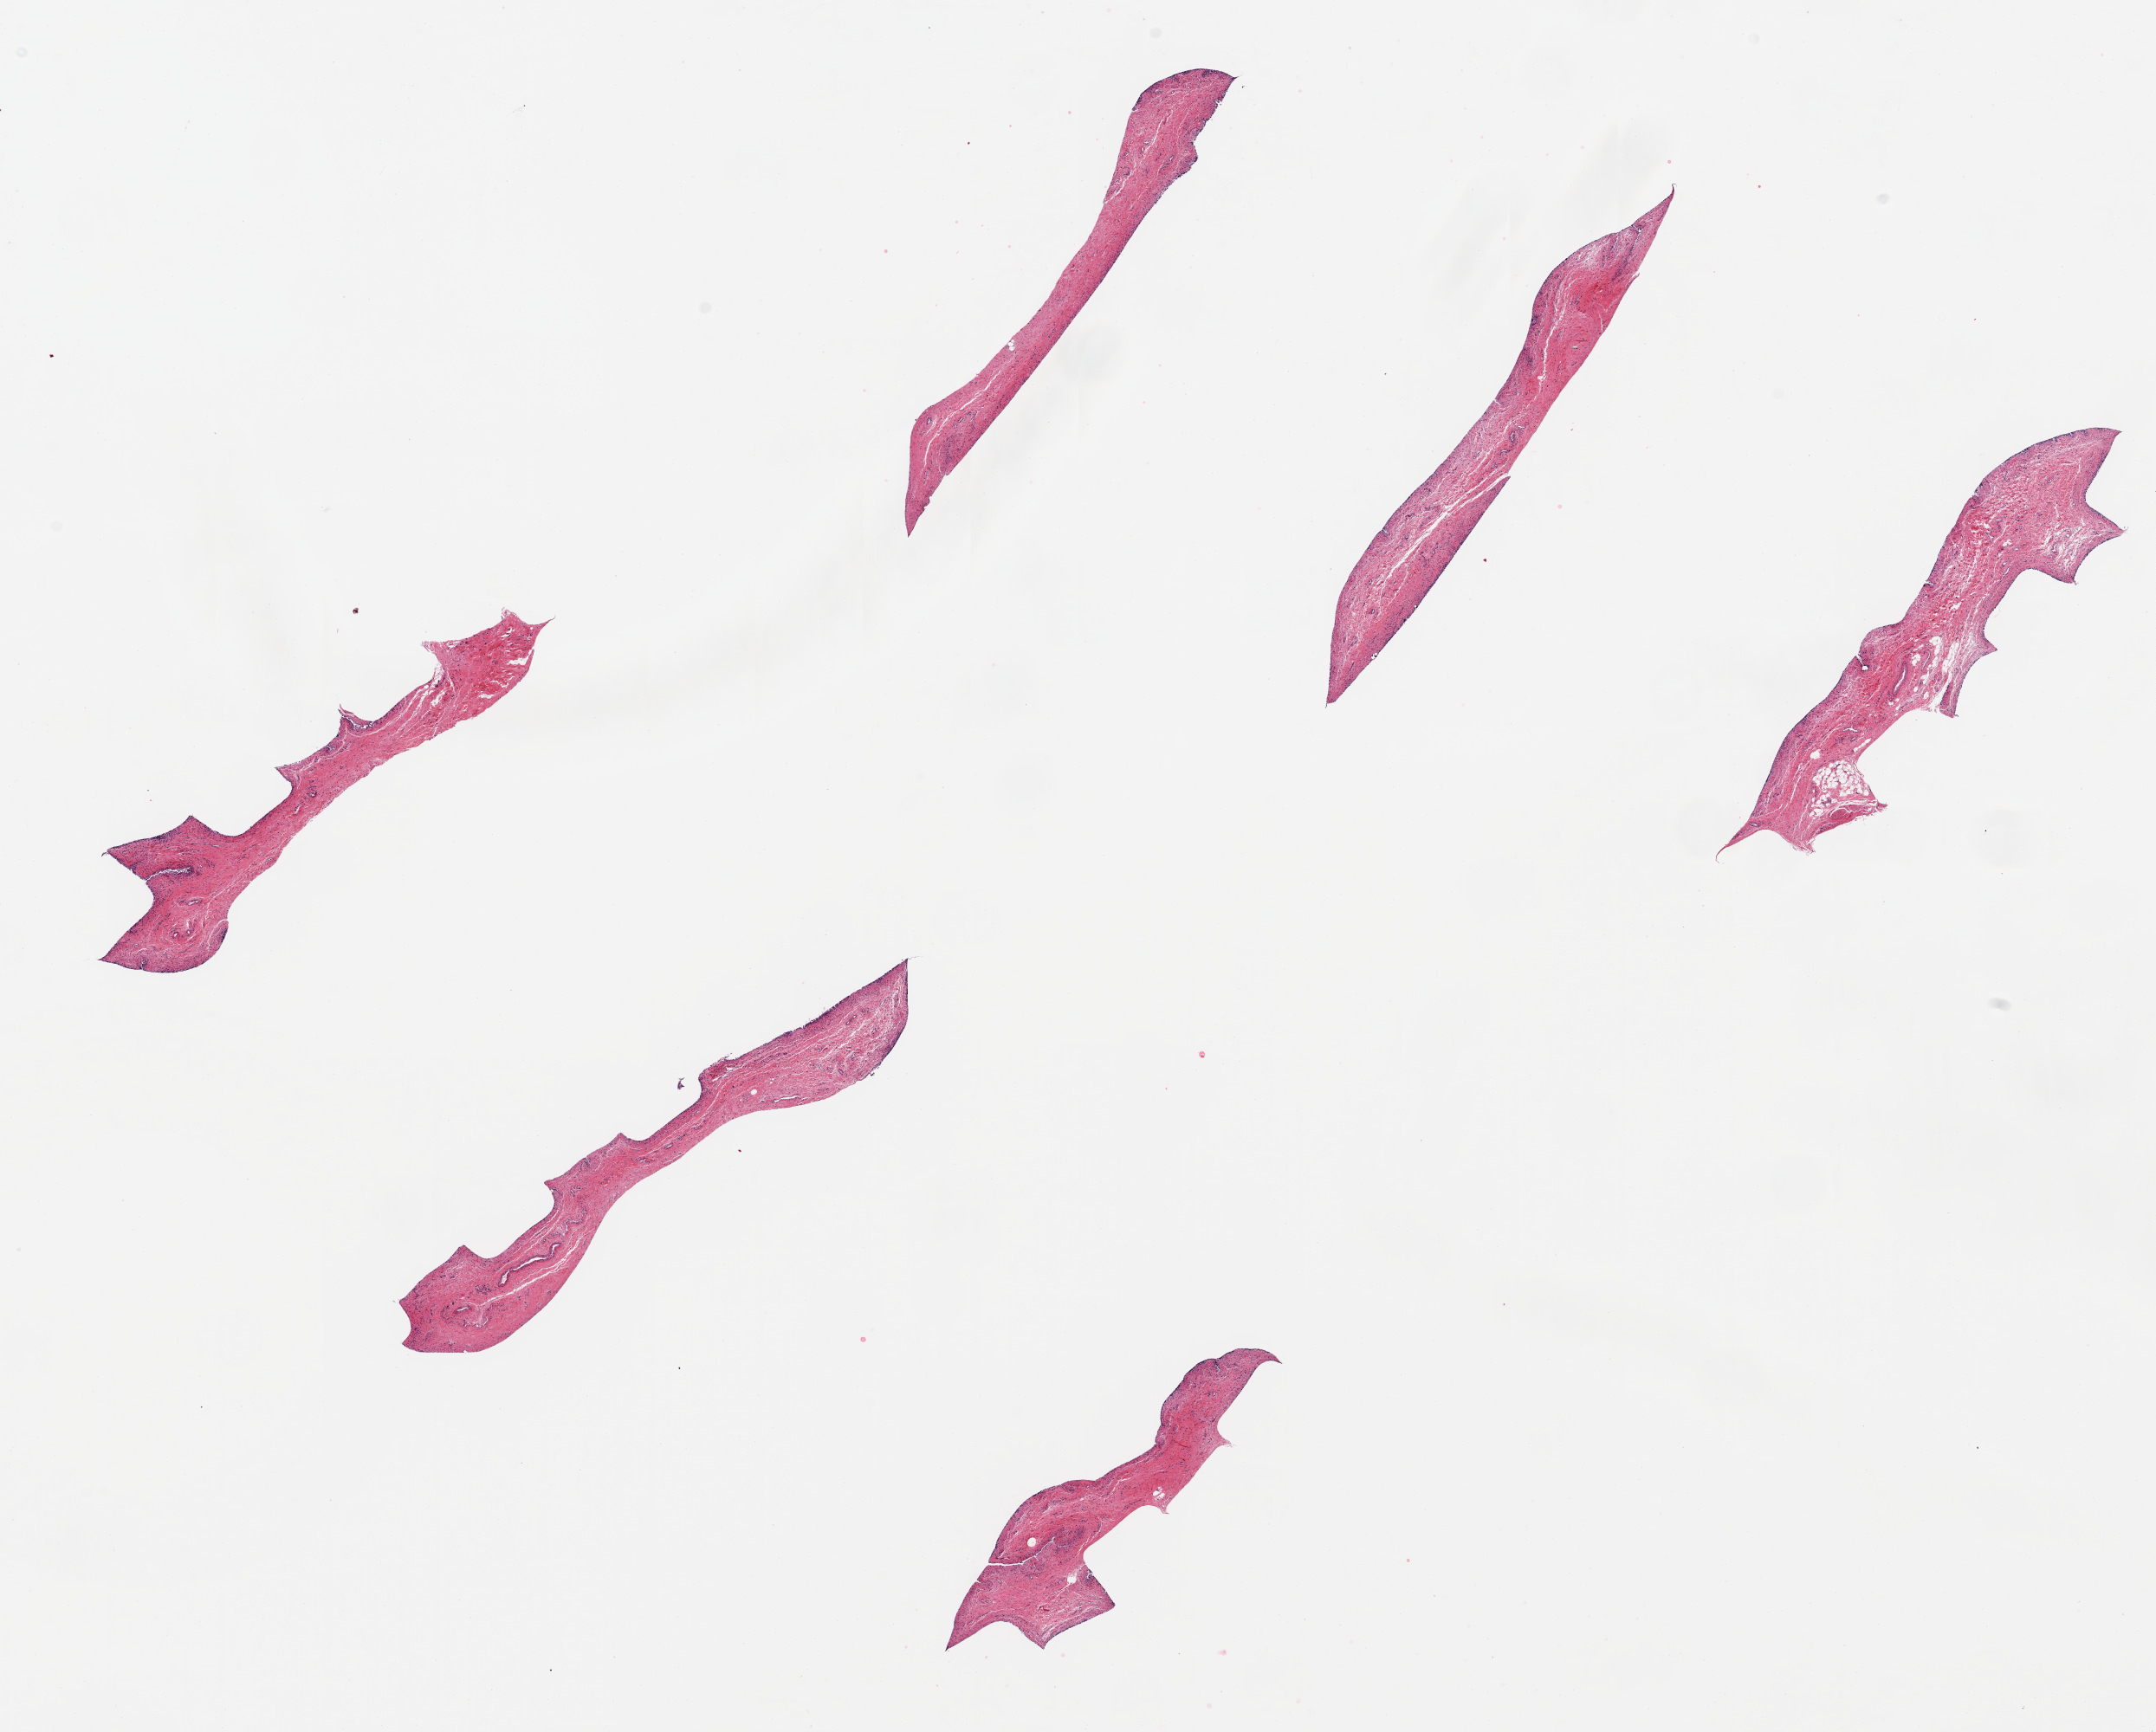
Whole-slide image, H&E stain, brightfield — a low-resolution overview of the entire scanned area, about 19.7 x 15.8 mm (acquisition: 20x scan); PAXgene-fixed, paraffin-embedded tissue; sampled site (target tissue): urinary bladder; tissue donor sample.
Pathologist's review note for this sample: 6 thin pieces up to 5.7x1.2 mm; epithelium largely sloughed; thin aliquot with no muscle; cassette ridge markings suggest tight fit.